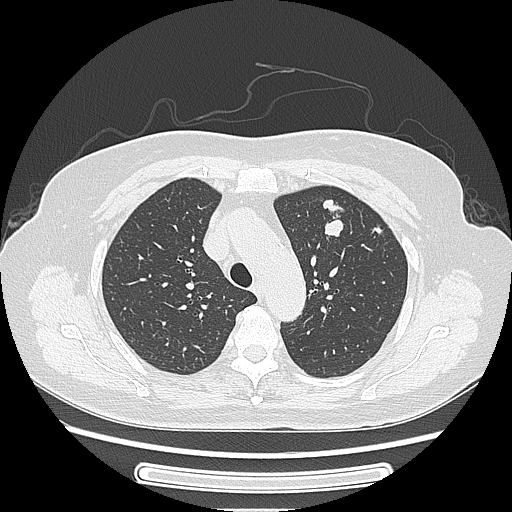
Chest CT, one axial slice; slice 177 of 227 in the series (ordered by position); 120 kVp; lung window (W 1500 / L -600 HU); 512 × 512 image matrix. Patient: female, 77 years. Case-level facts recorded for this patient, not image findings: clinical TNM (as recorded): T1c N3 M0; histopathological grade: G2-3.
Structures marked on this image (rectangle marked by the reading radiologist):
- lung tumour (recorded histology: adenocarcinoma): bounding box [x1, y1, x2, y2] px = [315, 193, 343, 245]